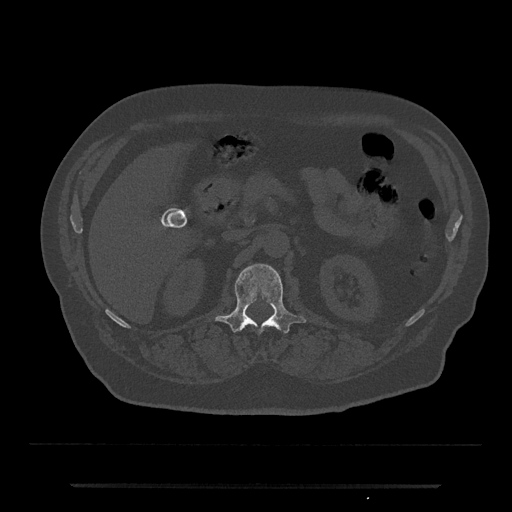
CT including the spine, one axial slice; slice 542 of 797 in the series (ordered by position); reconstruction kernel Br40s/3; bone window (W 1800 / L 400 HU); 0.5 mm slice thickness; 512 × 512 image matrix, field of view 434 × 434 mm. Patient: male, 80 years. From the clinical record (not read from this slice): primary cancer: prostate; vertebrae with lytic lesions (as recorded): L1, T11.
Structures marked on this image (semi-automatically segmented with operator editing):
- L1 vertebra: bounding box (x1, y1, x2, y2) in pixels: (215, 263, 306, 333)